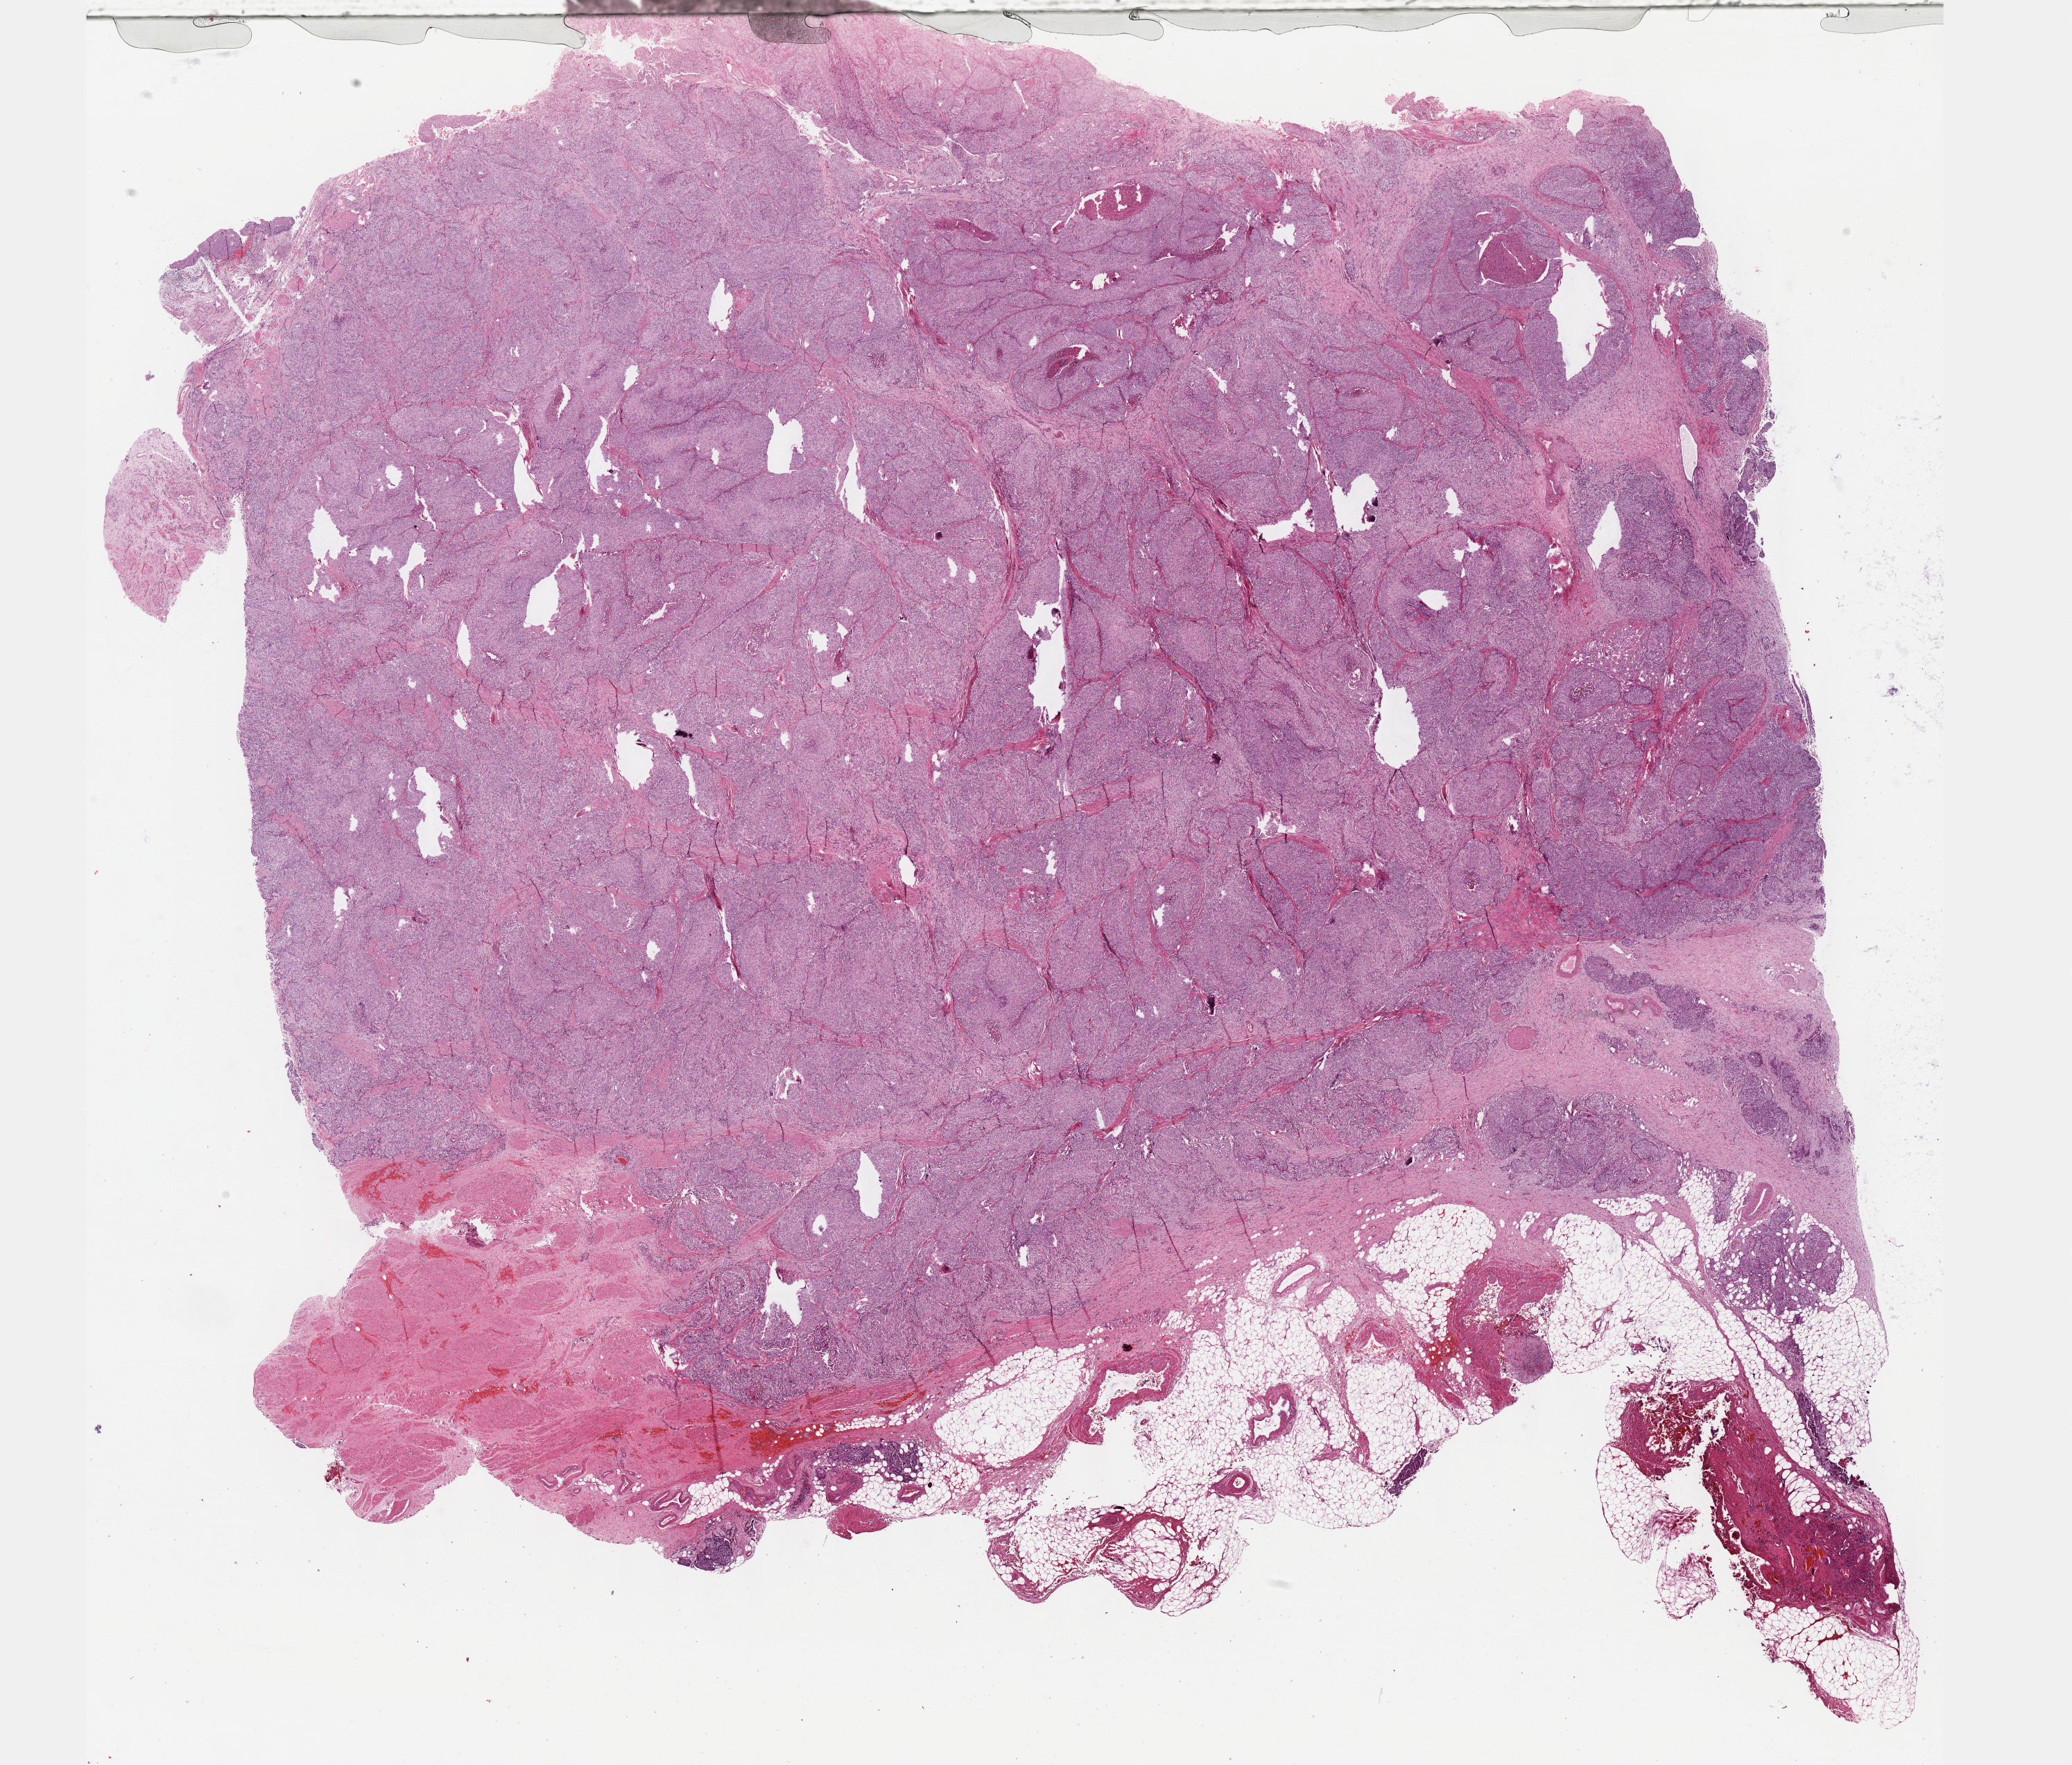
Whole-slide histology image, H&E, whole scanned area (about 24.1 x 20.6 mm, acquisition: 40x scan) shown as a low-resolution overview; FFPE section; primary tumour sample from the bladder. Male patient; age at initial diagnosis 85 years. Histologic grade: high grade.
• AJCC pathologic stage: III (6th edition)
• TNM: T3b N0 M0
• diagnosis: Papillary transitional cell carcinoma